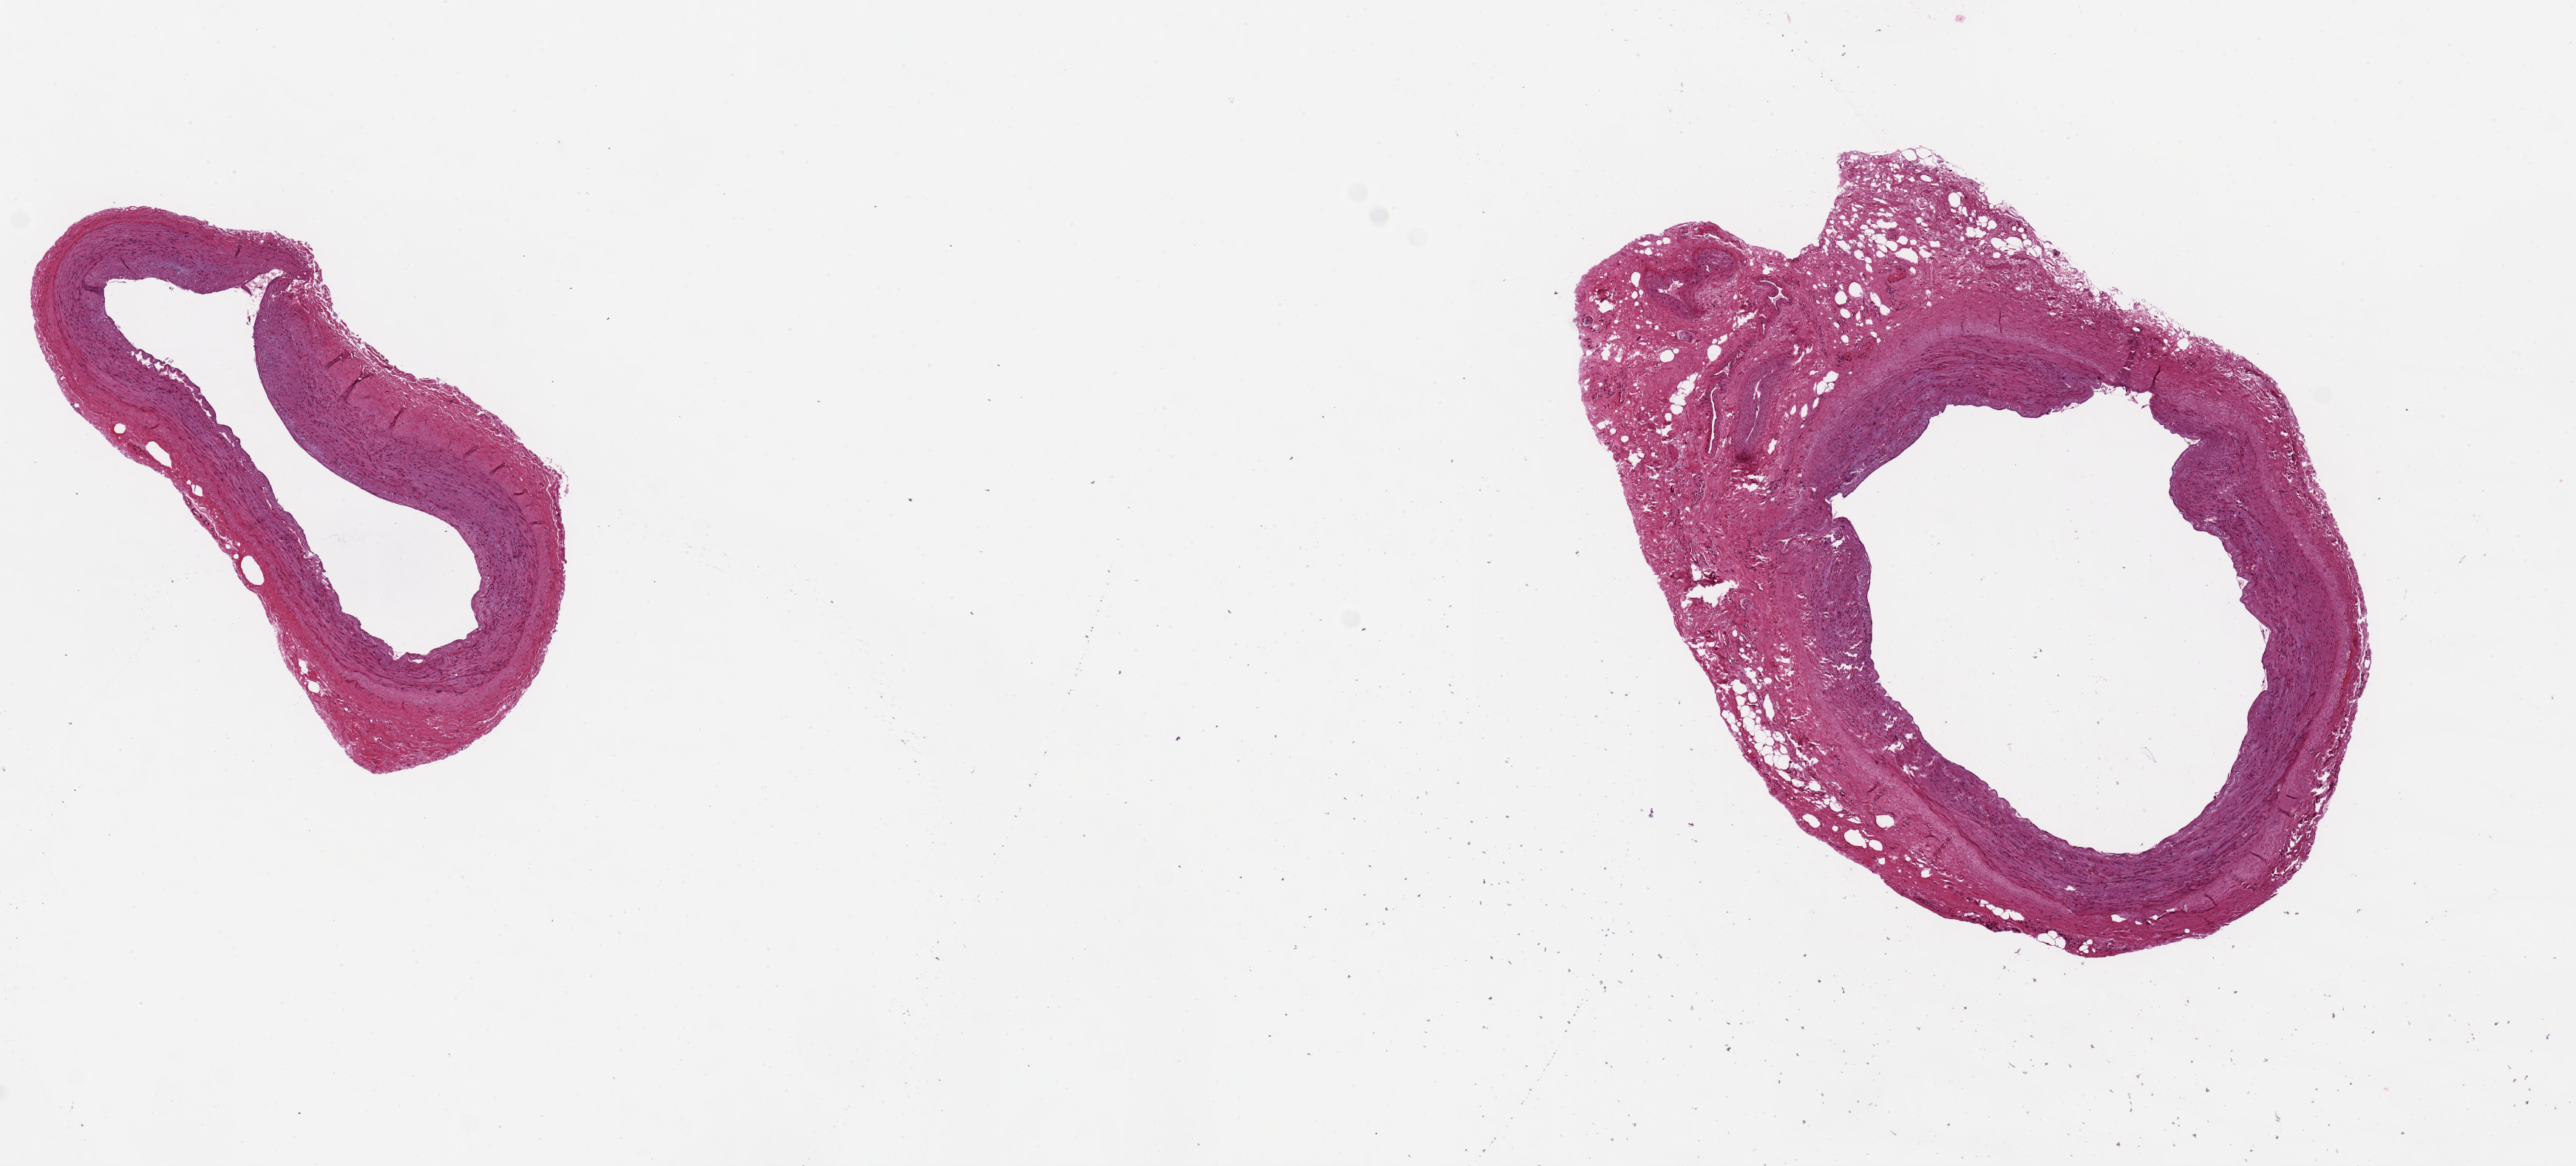
Digitized haematoxylin and eosin-stained section — low-resolution overview of the scanned area, about 13.8 x 6.2 mm (slide scanned at 20x); PAXgene-fixed, paraffin-embedded tissue; sampled site (target tissue): tibial artery; tissue donor sample. Donor sex: female.
* pathologist's review note for this sample: 2 pieces: 4.9x3.4mm; 3.5x1.4mm